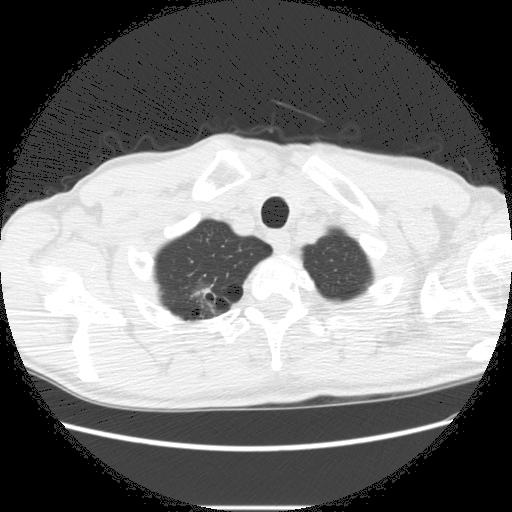
Low-dose screening chest CT, one axial slice; slice 262 of 282 in the series (ordered by position); reconstruction kernel STANDARD; lung window (W 1500 / L -600 HU); 512 × 512 image matrix, field of view 360 × 360 mm.
Annotated regions visible in this slice (outlined manually by an expert reader):
- lesion 2 (nodule, upper lobe of right lung): bounding box (x1, y1, x2, y2) in pixels: (200, 289, 217, 306)